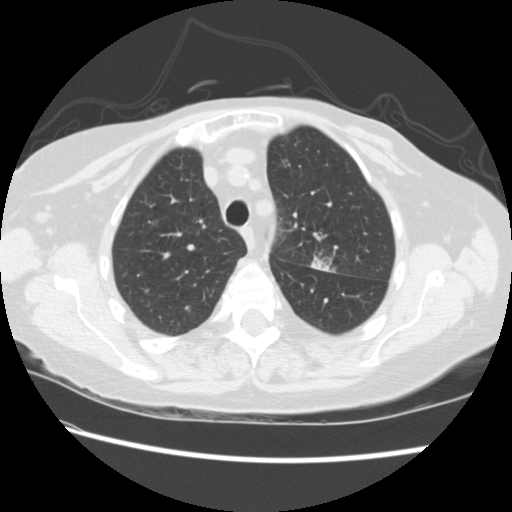
Low-dose screening chest CT, one axial slice; position 167 of 224 along the scan axis; 120 kVp; lung window (W 1500 / L -600 HU); 2.5 mm slice thickness; 512 × 512 image matrix, field of view 340 × 340 mm.
Annotated regions visible in this slice (manually delineated by an expert):
- lesion 1 (tumor, upper lobe of left lung): bounding box (x1, y1, x2, y2) in pixels: (311, 257, 332, 272)